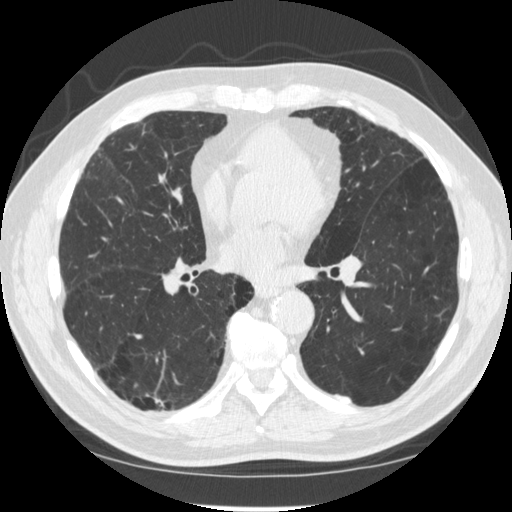
Low-dose screening chest CT, axial slice. Second screening round (one year after baseline). Lung window (W 1500 / L -600 HU). 1.25 mm slice thickness. Slice 150 of 303 in the series. 512 × 512 image matrix. Male participant, aged 70 years at enrolment. Former smoker at enrolment.
• Expert reader's lesion annotation, bounding box (x1, y1, x2, y2) in pixels: (130, 378, 181, 429).
• The screening reader recorded 2 non-calcified nodules or masses ≥4 mm on this exam (right lower lobe, right lower lobe); which of them this box marks is not recorded.
• Official screen result: negative screen, significant abnormalities not suspicious for lung cancer.
• Lung cancer was diagnosed 617 days after this screen (after the third annual screen): squamous cell carcinoma, NOS, right upper lobe, poorly differentiated (G3), stage IV (AJCC 6th edition).